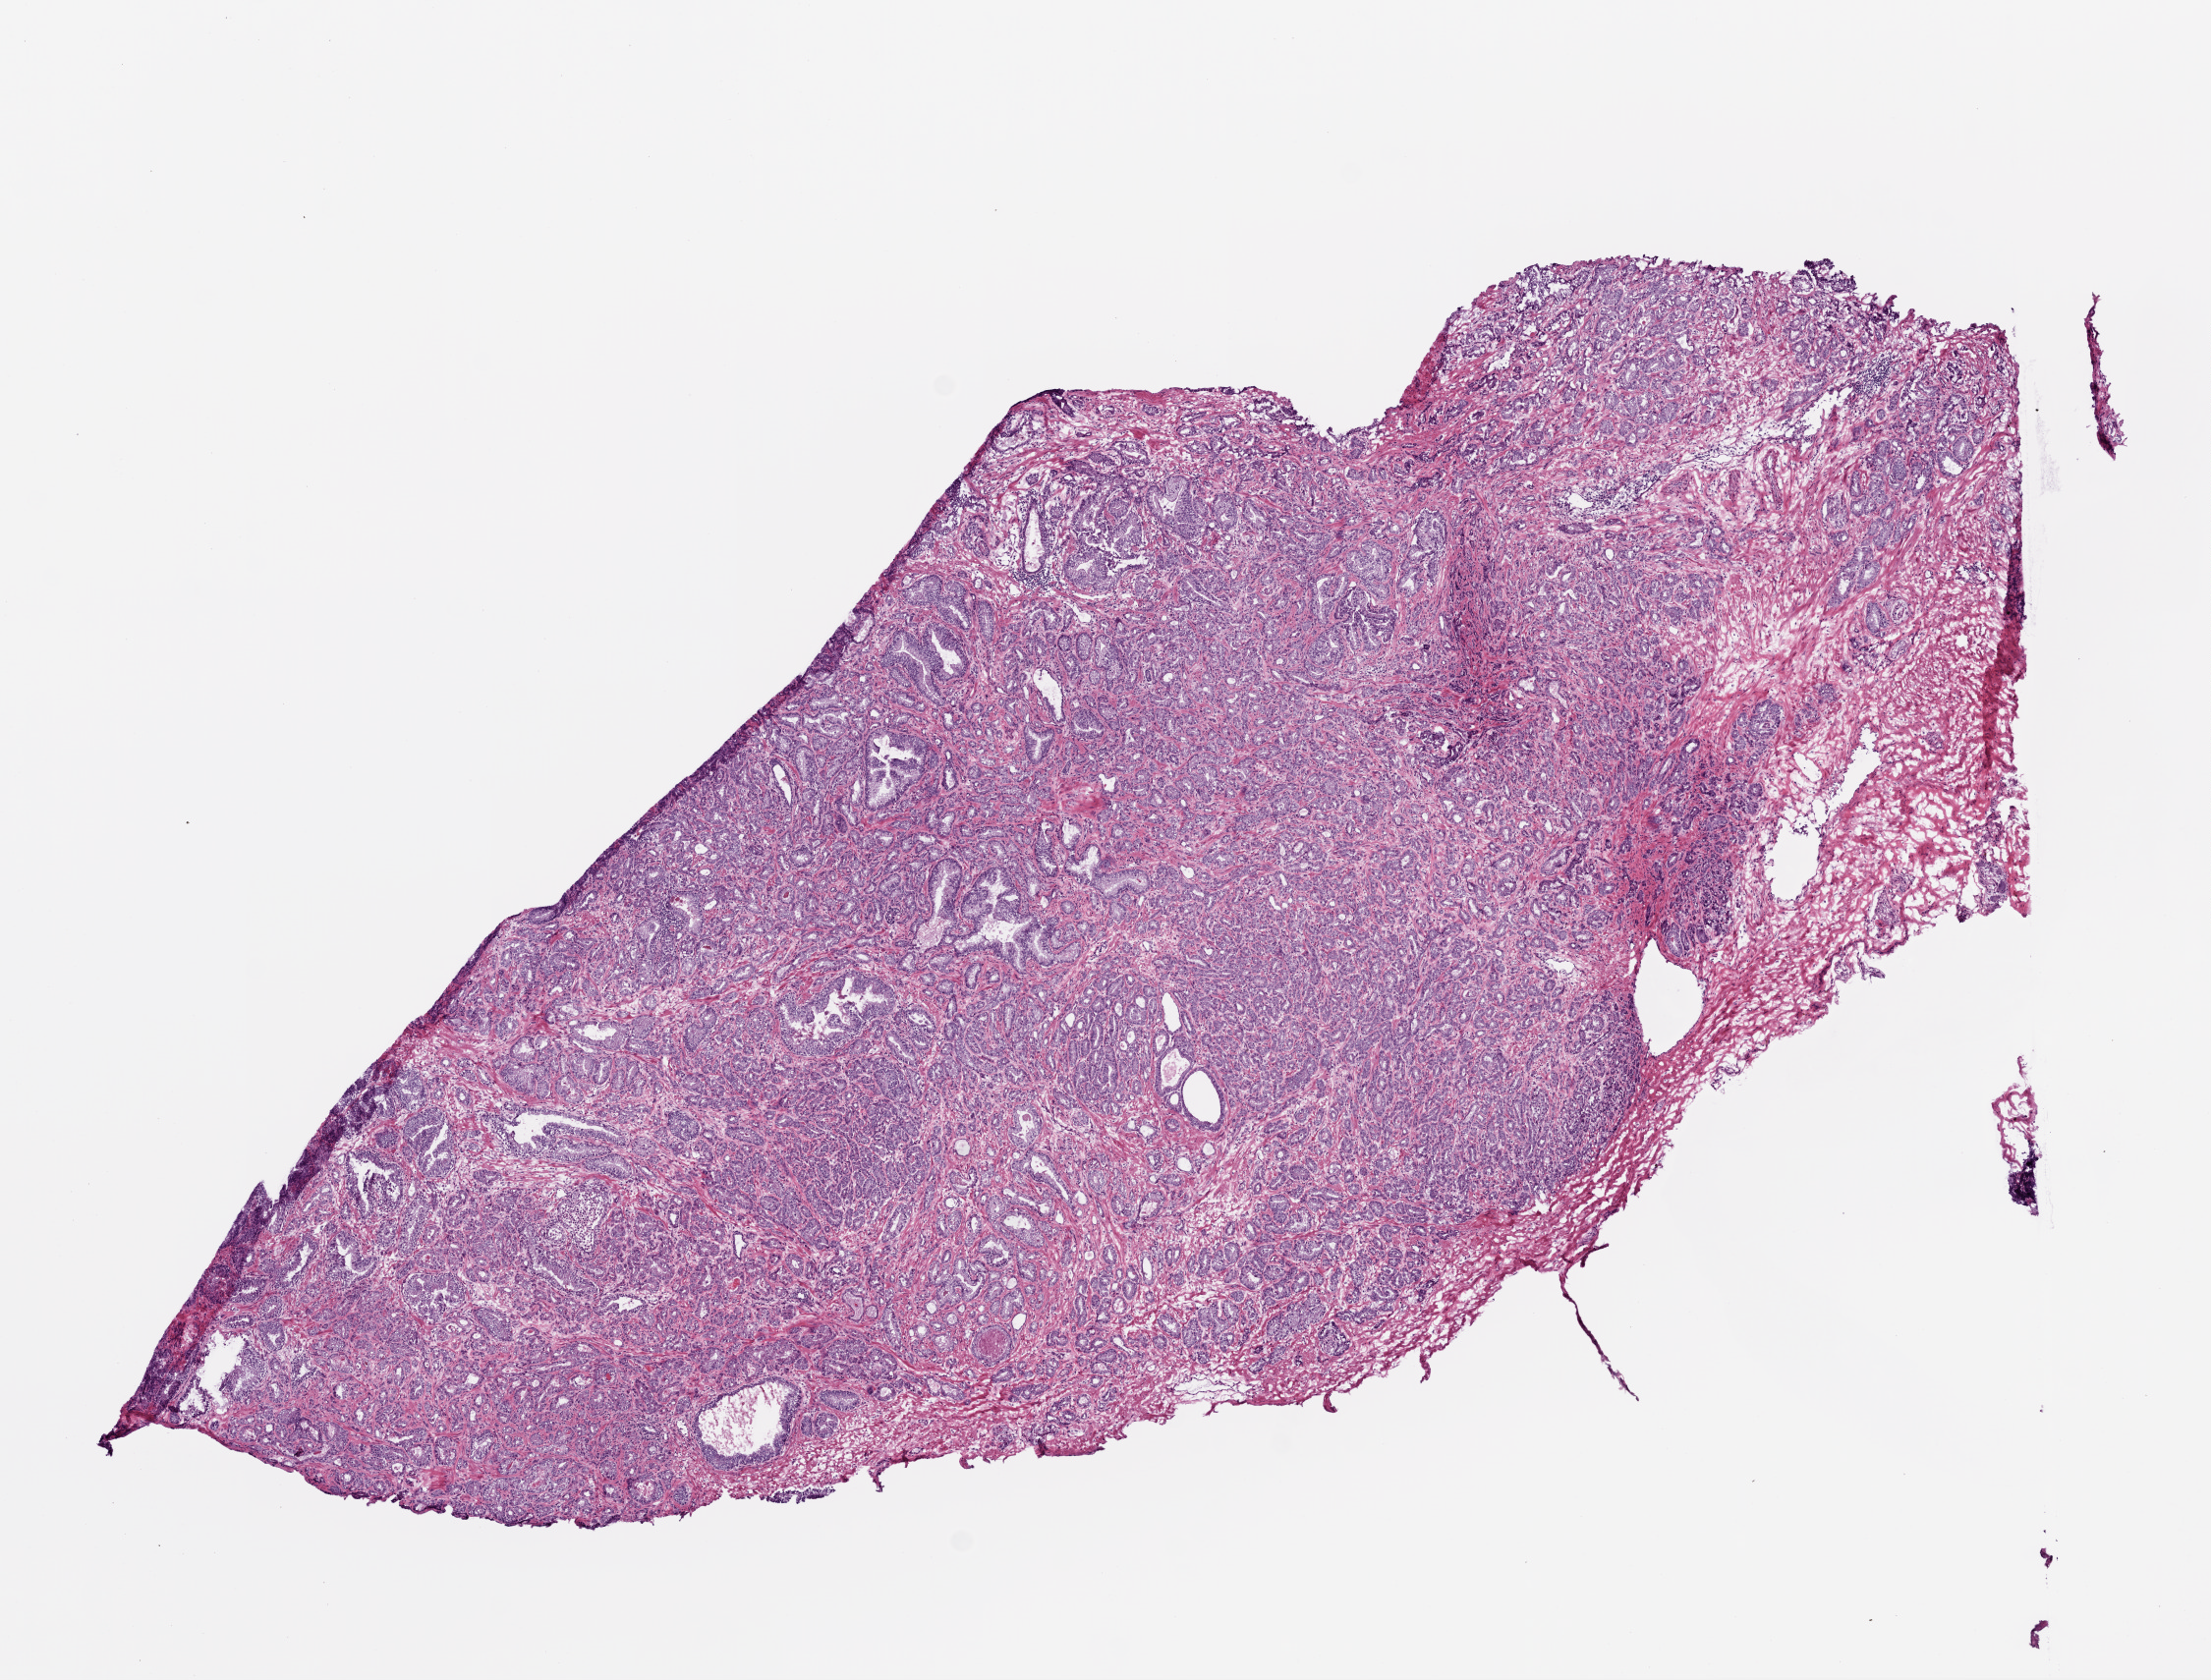
Whole-slide histology image, H&E, low-resolution overview of the scanned area, about 9.0 x 6.9 mm; frozen section from the top of the tissue portion; primary tumour sample from the prostate. Male patient; age at initial diagnosis 64 years. Gleason score: 7 (4+3). Pathologist review of this section (percent, as recorded): tumour cells 75%, tumour nuclei 80%, normal cells 10%, stromal cells 15%, necrosis 0%. Infiltration values recorded for this section: lymphocyte infiltration 0%, monocyte infiltration 0%, neutrophil infiltration 0%.
Lymph nodes positive (case pathology): 0 of 2 examined. Diagnosis: Acinar cell carcinoma (prostate gland). Laterality: bilateral.